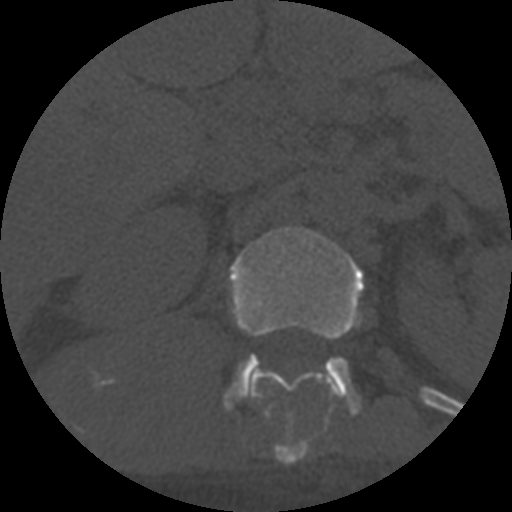
CT including the spine, one axial slice; slice 299 of 708 in the series (ordered by position); 120 kVp; one of 3 acquisitions stored at this slice position; bone window (W 1800 / L 400 HU); 1.25 mm slice thickness; 512 × 512 image matrix, field of view 160 × 160 mm. Patient age 55 years. From the clinical record (not read from this slice): primary cancer: colon; vertebrae with lytic lesions (as recorded): T12, L1, L5.
Outlined on this slice (semi-automatically segmented with operator editing):
- L1 vertebra: box from (x=225, y=226) to (x=365, y=414) px
- T12 vertebra: (x=249, y=370)–(x=330, y=464)